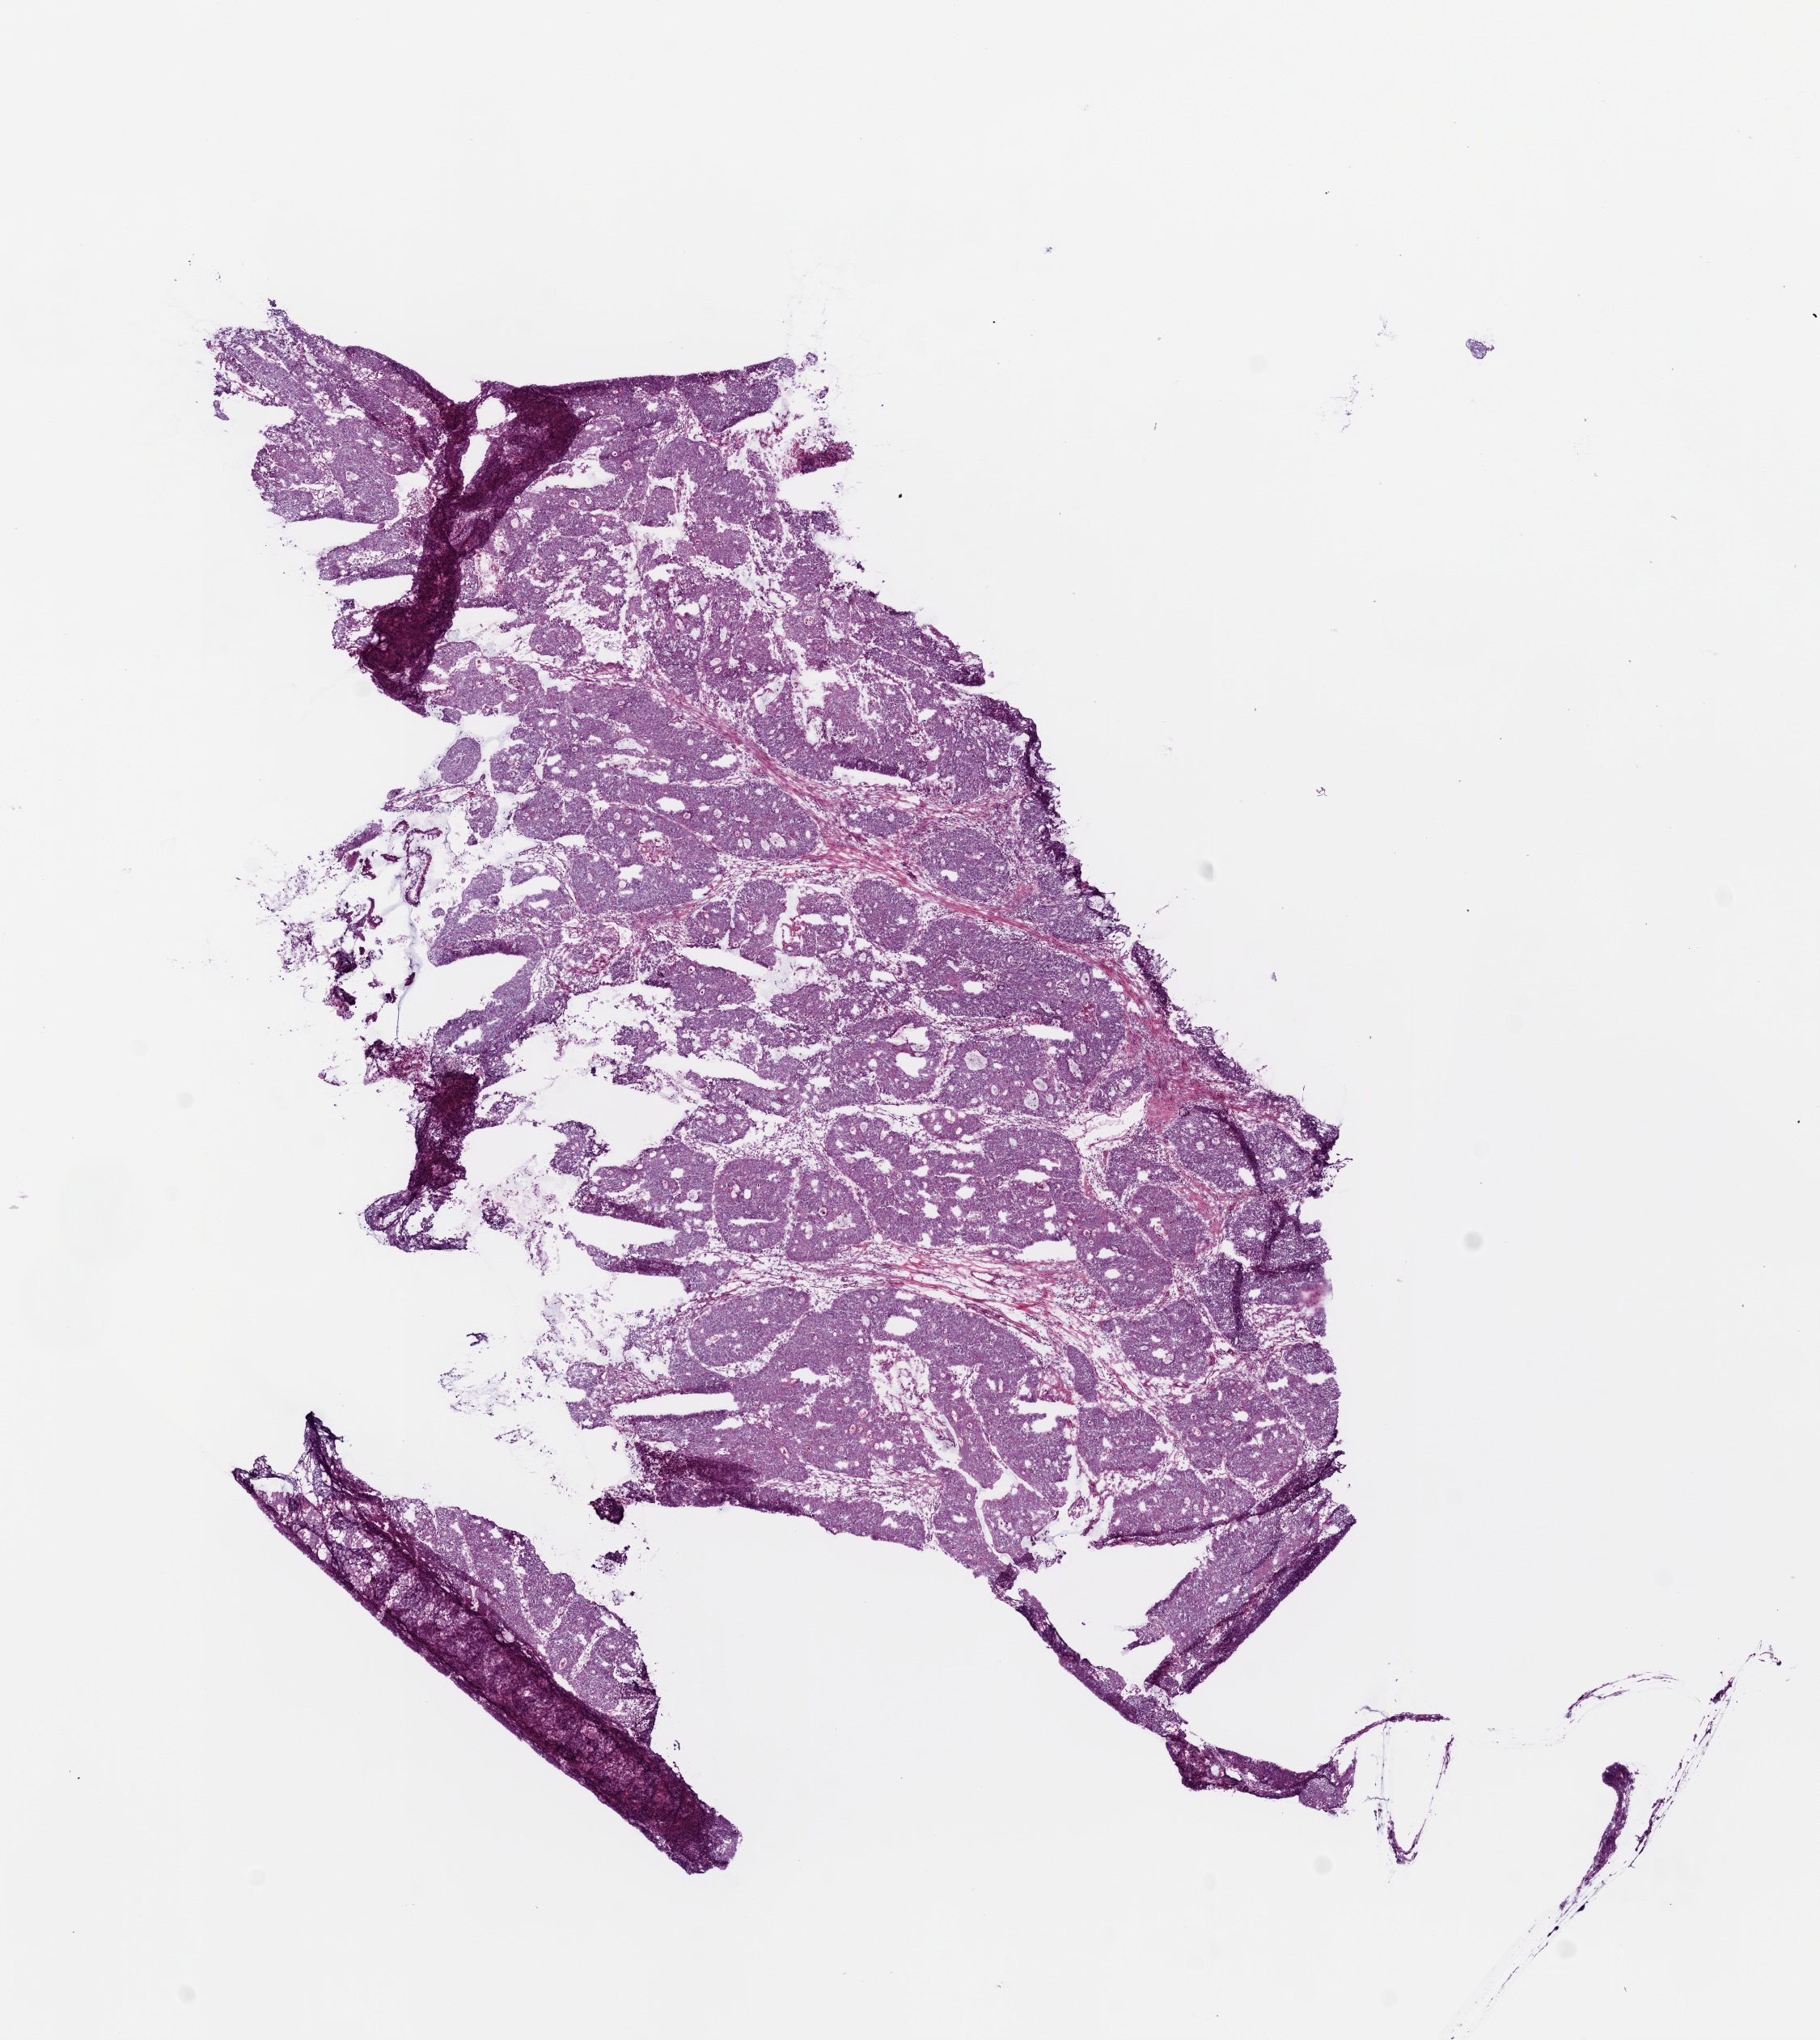
Whole-slide histology image, H&E, low-resolution overview of the scanned area, about 9.0 x 10.1 mm, frozen section from the bottom of the tissue portion, sample: primary tumour, rectum. Female, age 72 years at initial diagnosis. Slide review estimates, as recorded: tumour cells 87%, tumour nuclei 75%, normal cells 0%, stromal cells 5%, necrosis 8%.
Lymph nodes positive (case pathology): 4 of 19 examined. Pathologic diagnosis: Mucinous adenocarcinoma (rectosigmoid junction). AJCC pathologic stage: III (5th edition).